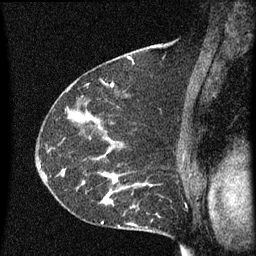
Breast MRI (dynamic contrast-enhanced), one sagittal slice. Position 40 of 60 along the scan axis. Dynamic contrast-enhanced series, image 2 of 3 at this slice position (ordered by acquisition). 1.5 T. TE 4.2 ms, TR 8 ms. 256 × 256 image matrix, field of view 180 × 180 mm. Patient: female, 55 years.
Annotated regions visible in this slice (semi-automatically segmented with operator editing):
- analysis volume of interest (the breast-tissue region the enhancement analysis was run in; not a lesion): box from (x=51, y=156) to (x=145, y=217) px
- tumour enhancement mask (voxels above the 70 % enhancement threshold inside the analysis volume of interest): (x=62, y=156)–(x=145, y=209)